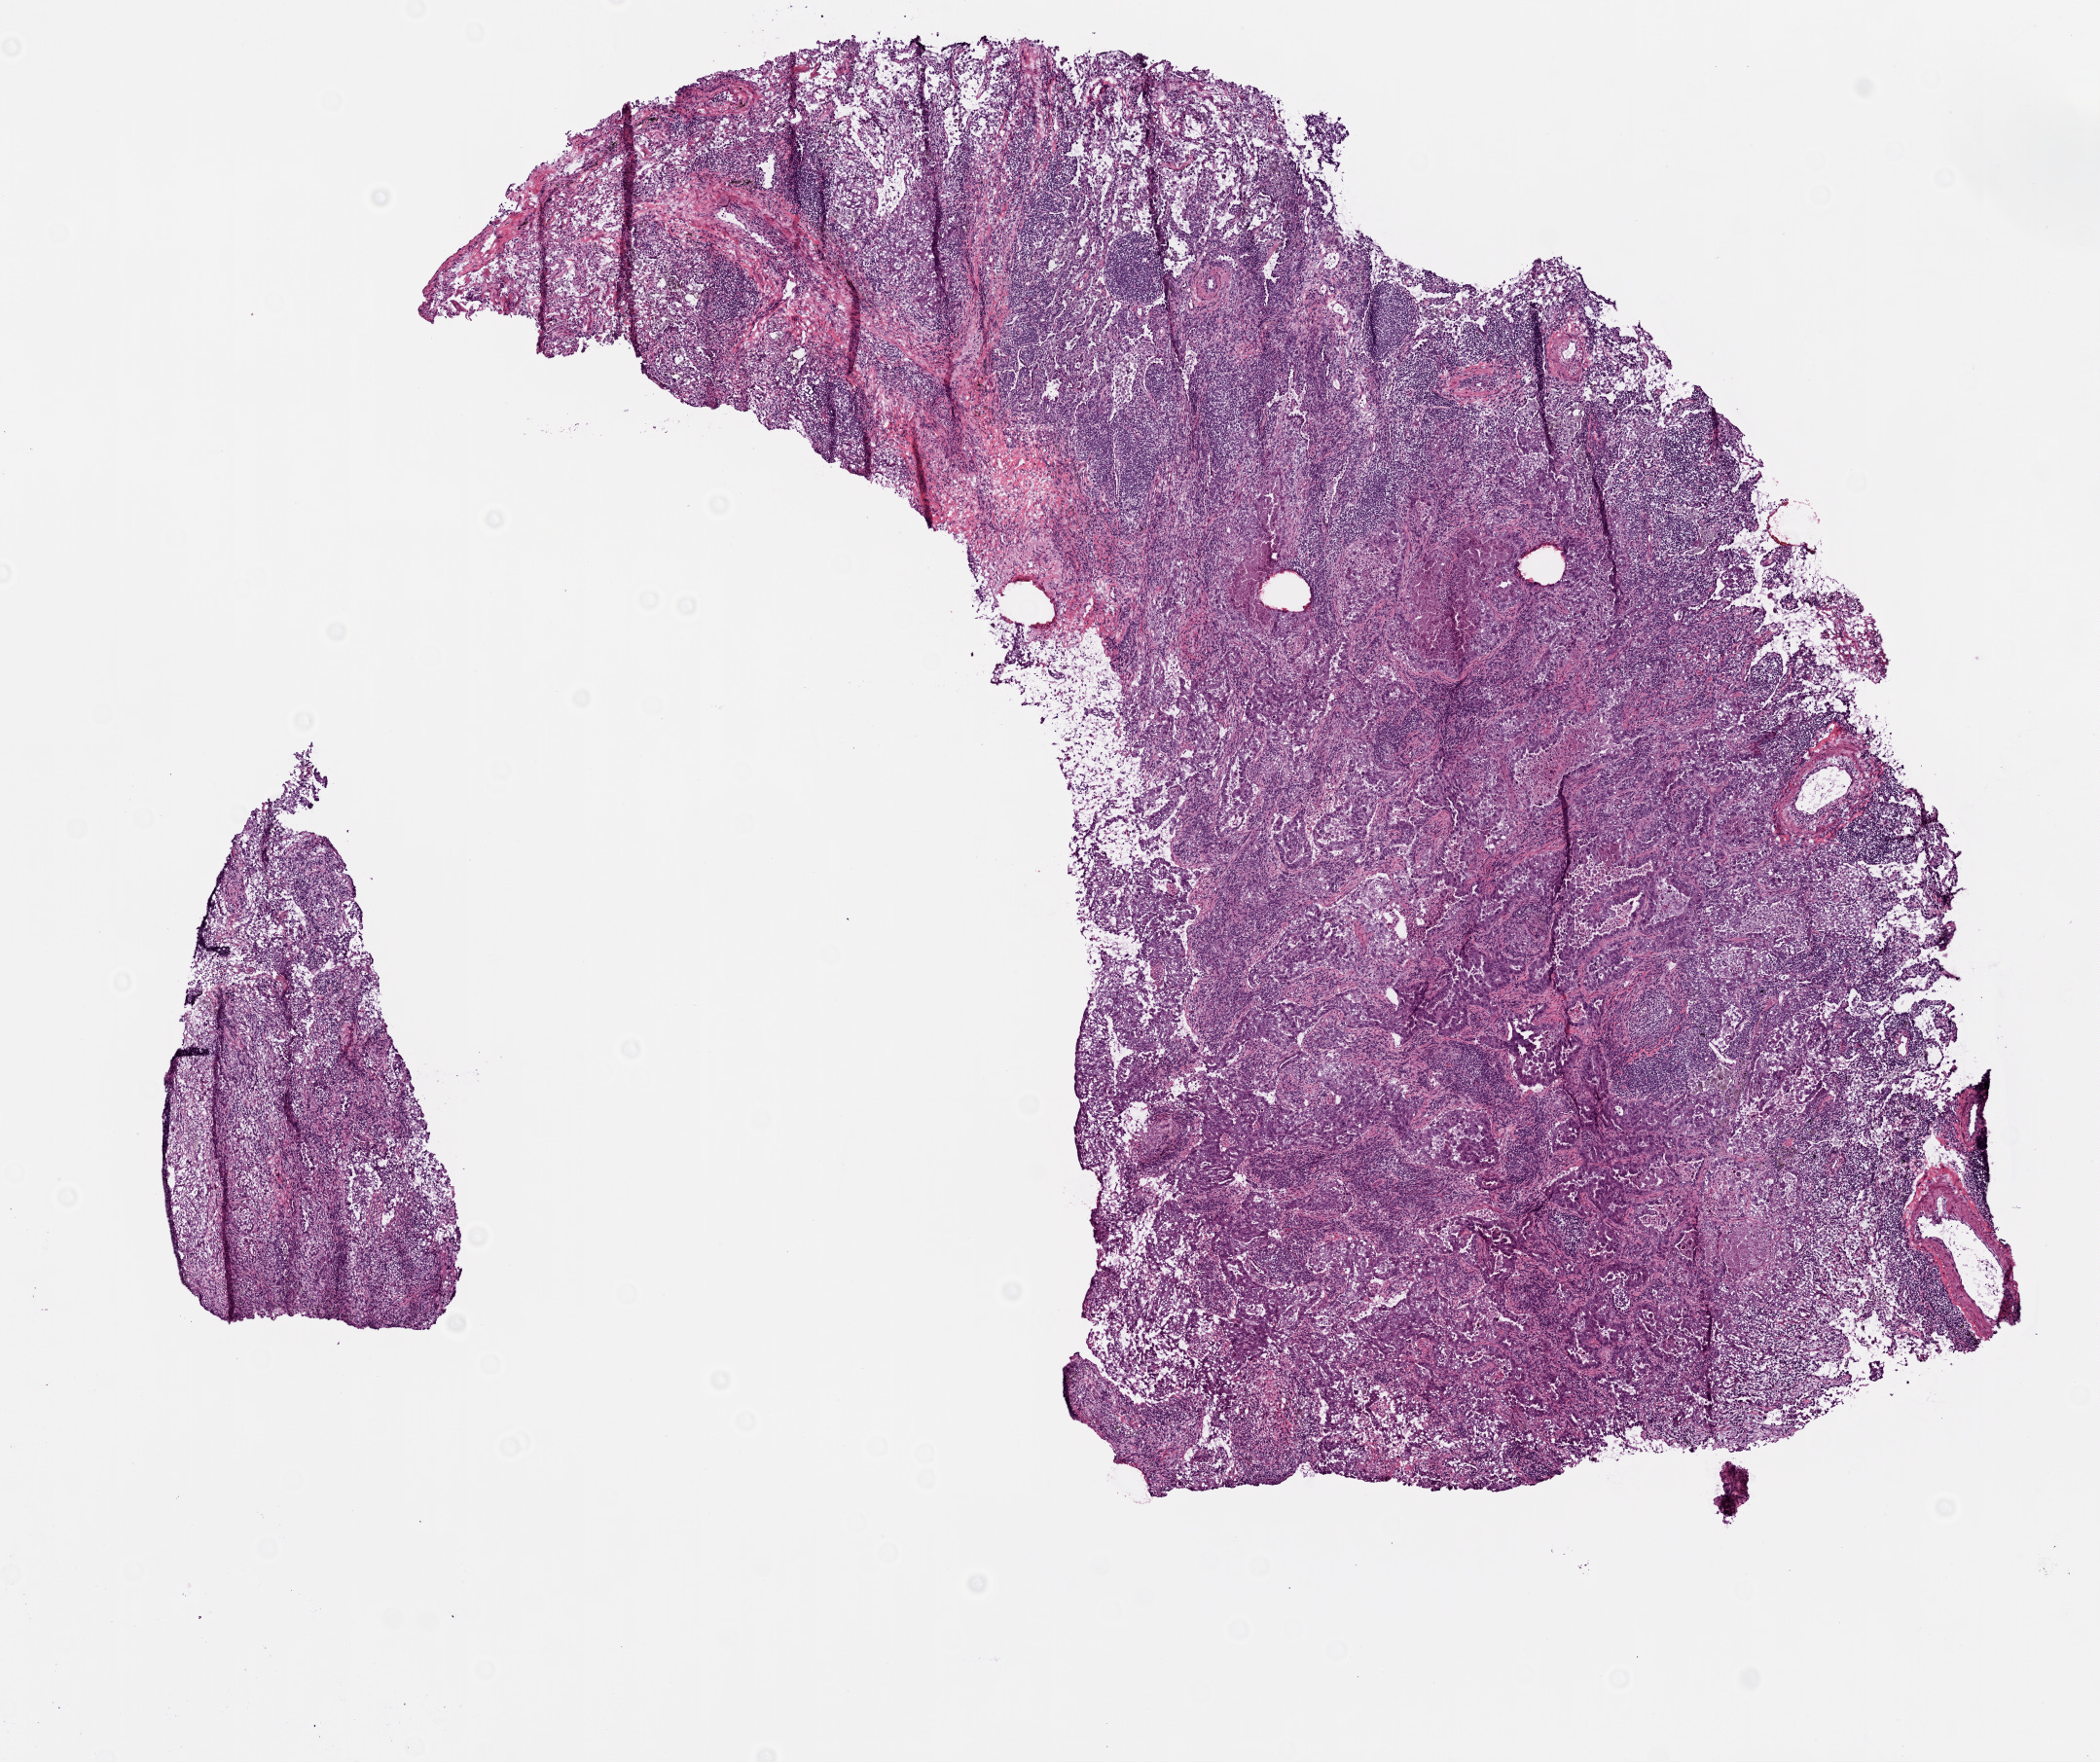
Whole-slide histology image, H&E — shown as a low-resolution overview of the whole scanned area (about 8.7 x 7.3 mm, slide scanned at 20x); frozen section; sample: primary tumour, lung. Female, age 52 years at initial diagnosis.
Pathologic diagnosis: Adenocarcinoma, NOS.